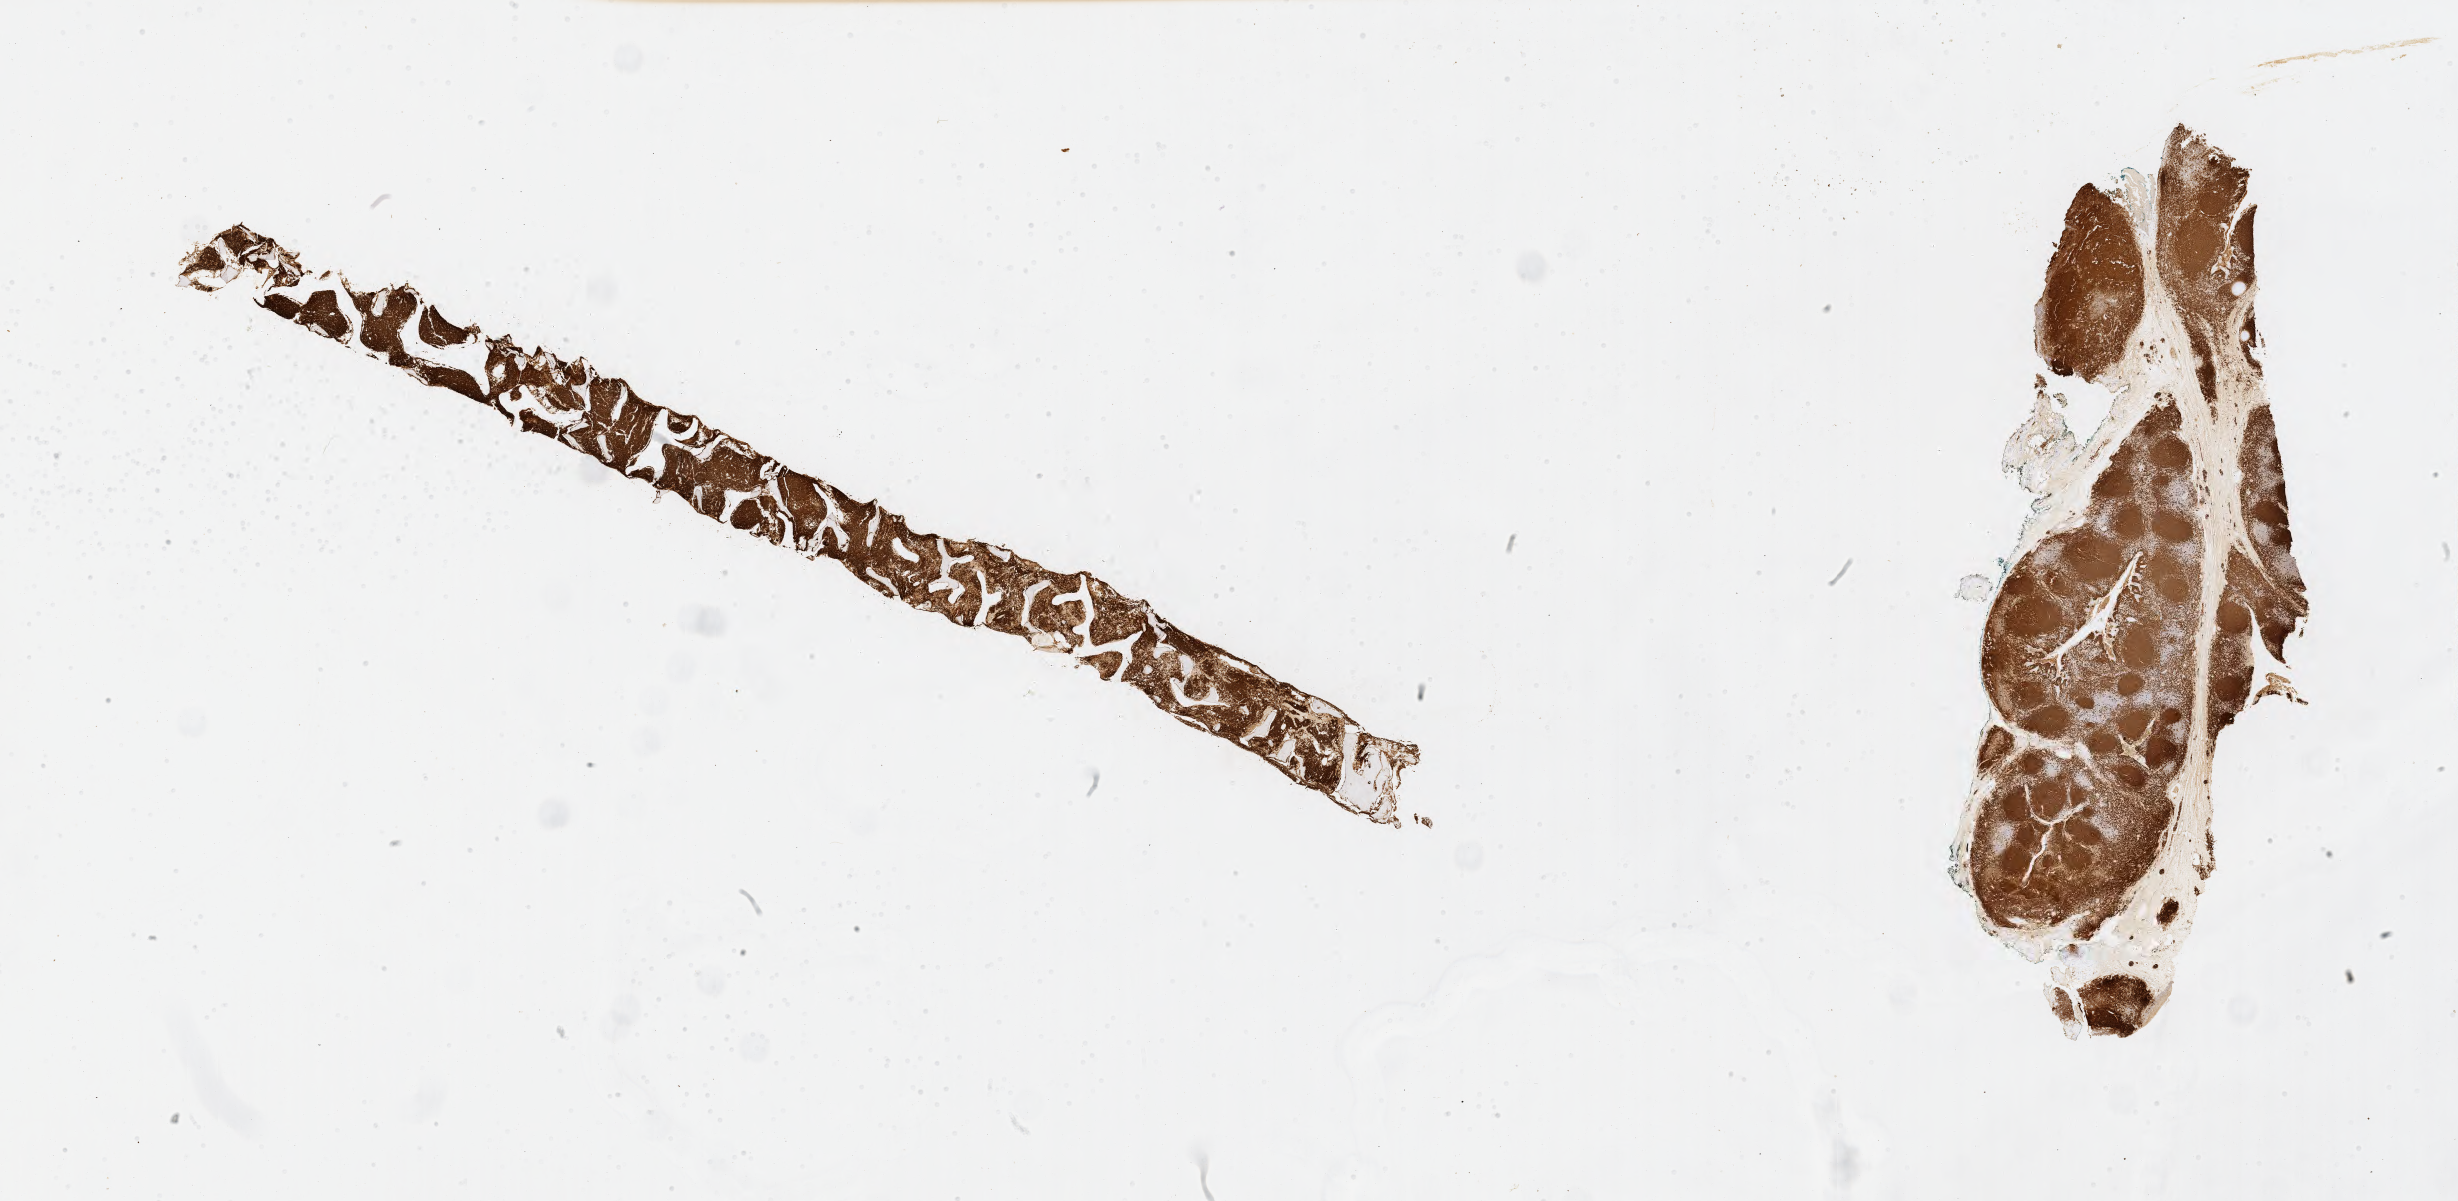
Immunohistochemistry (IHC) whole-slide image stained for CD20, a low-resolution overview of the entire scanned area, about 39.7 x 19.4 mm; specimen: tumor tissue; site: bone marrow. Patient: male, aged 18.
Diagnosis: Burkitt lymphoma, NOS.